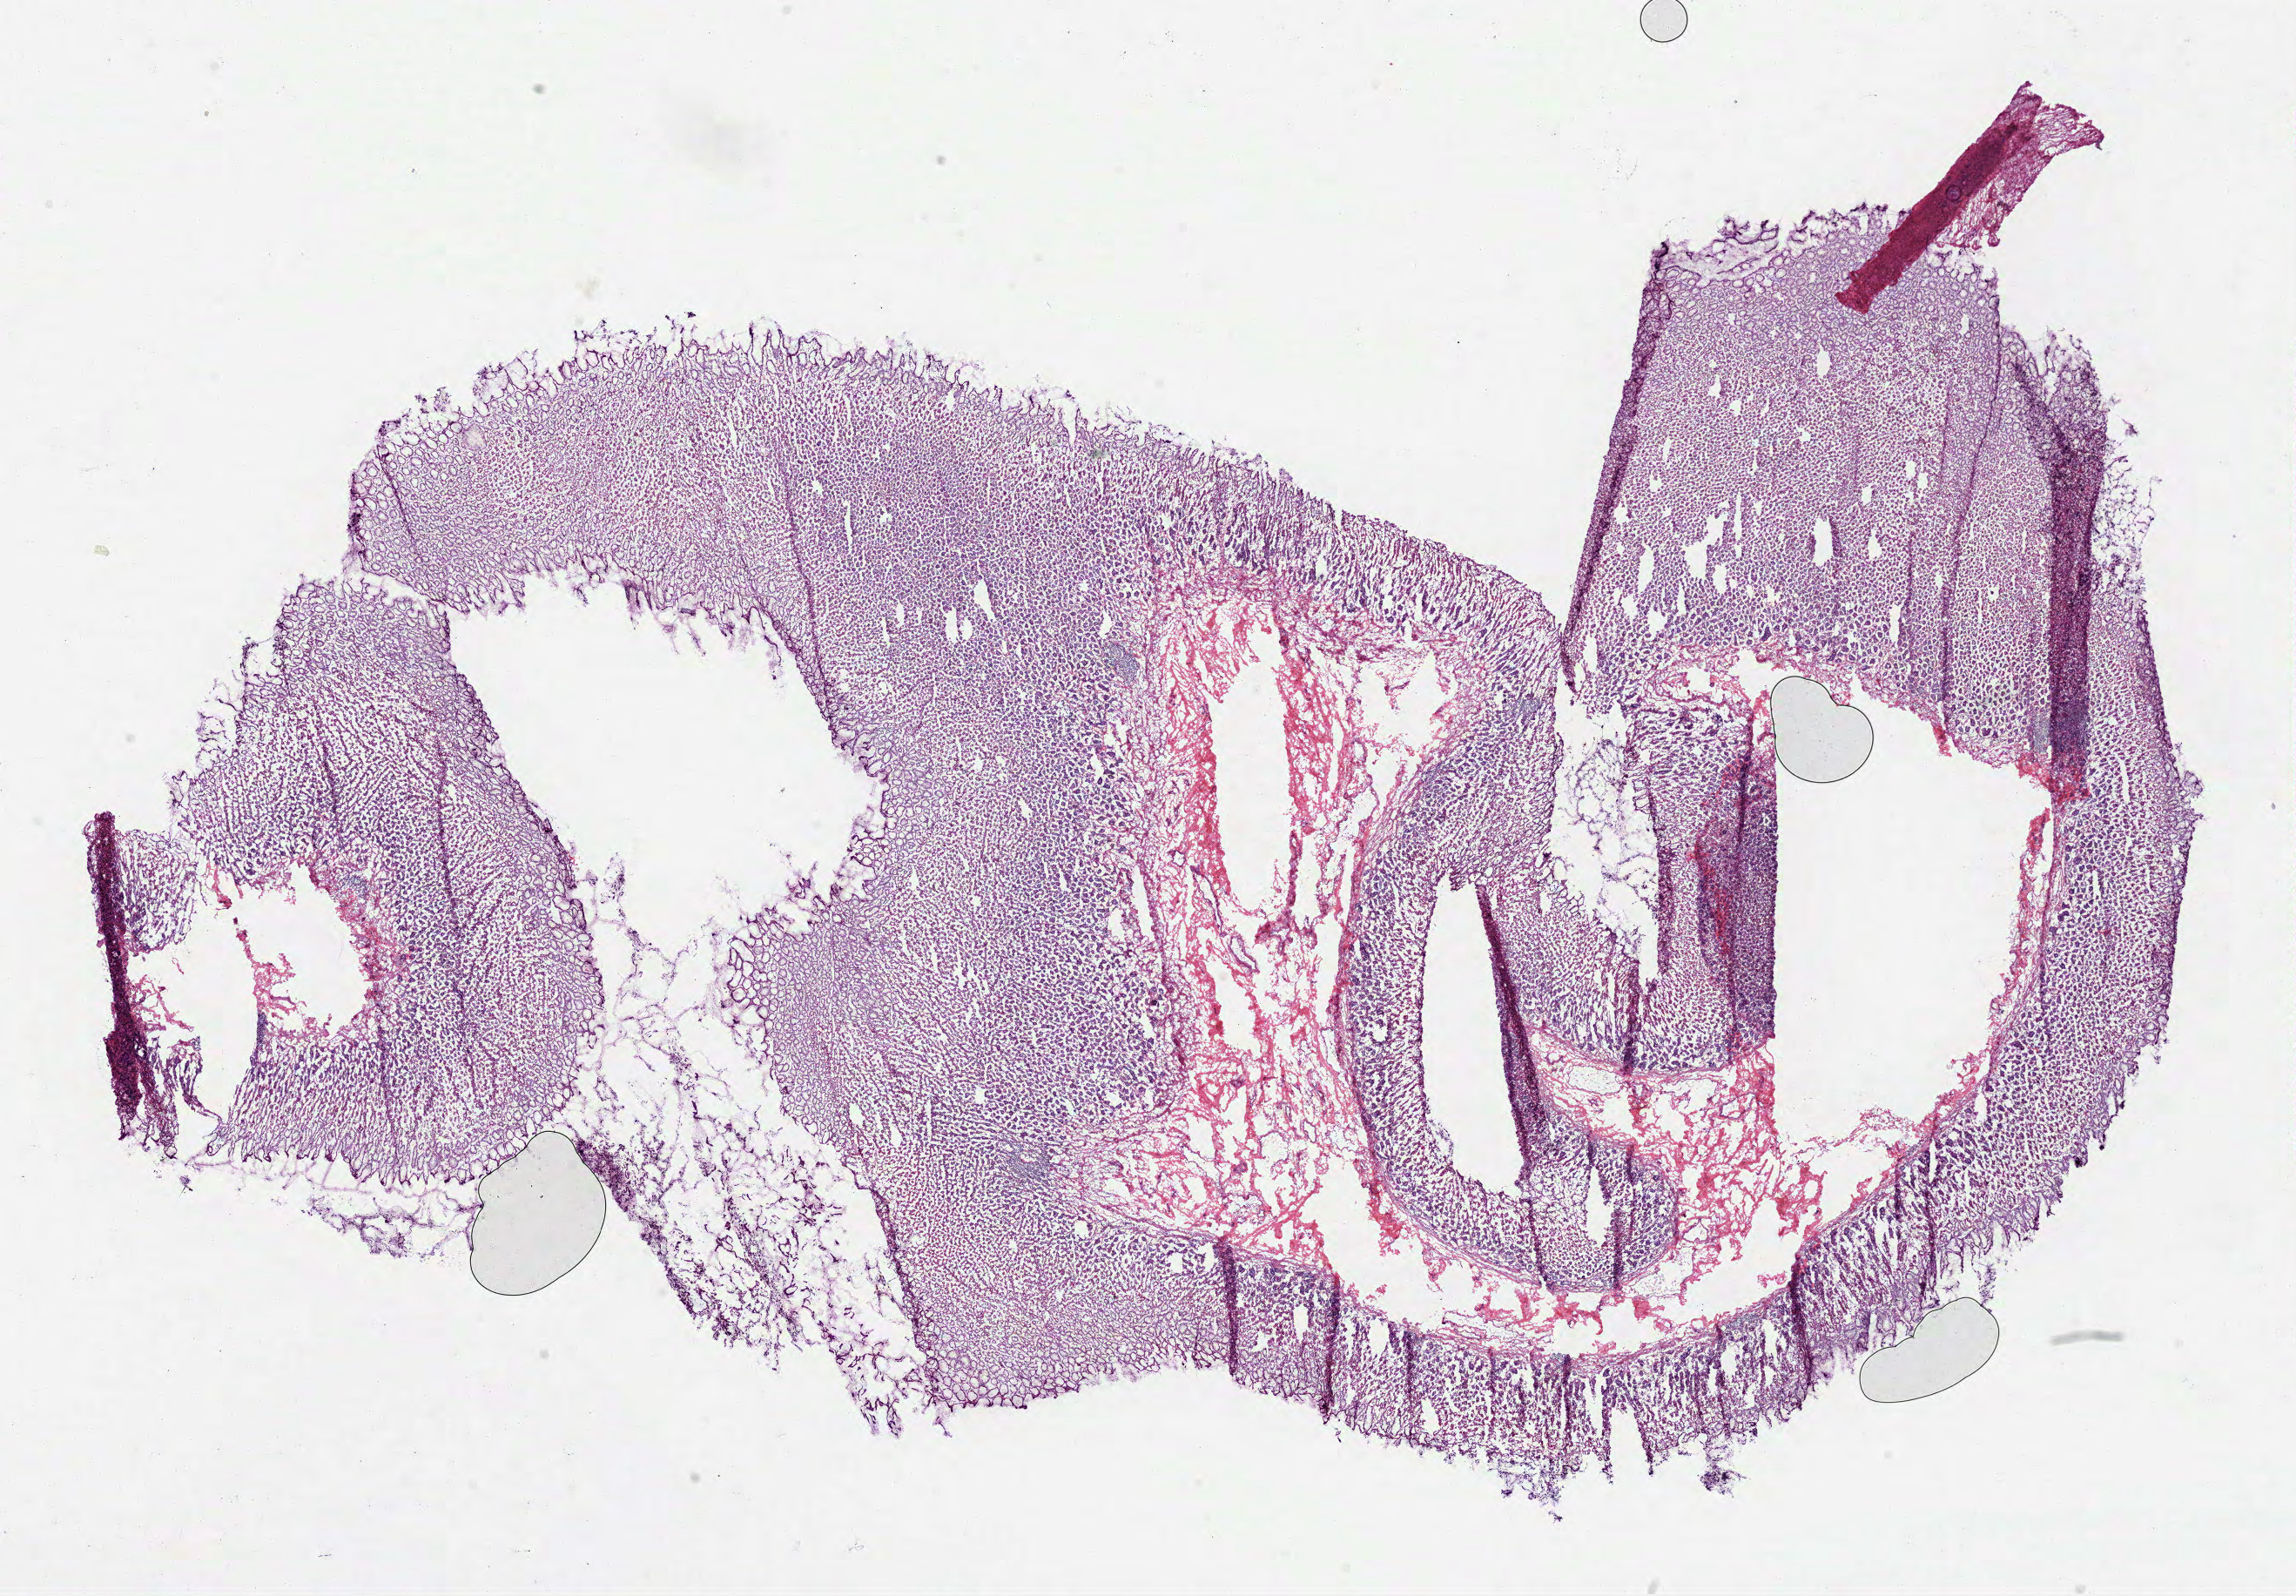
H&E whole-slide image — low-resolution overview of the scanned area, about 21.3 x 14.8 mm, frozen section, sample: solid tissue normal (non-tumour tissue), stomach. Female, age 50 years at initial diagnosis.
• this section: solid tissue normal sample (biorepository sample class)
• patient diagnosis: Adenocarcinoma, intestinal type (body of stomach)